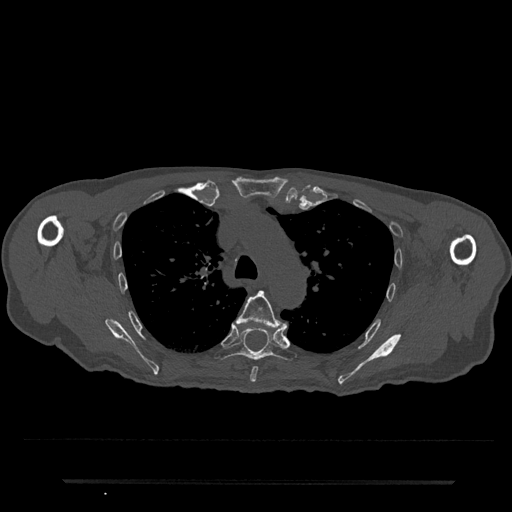
CT including the spine, one axial slice. Reconstruction kernel Br40s/3. Bone window (W 1800 / L 400 HU). 0.5 mm slice thickness. 512 × 512 image matrix. Male patient, age 74 years. From the clinical record (not read from this slice): primary cancer: prostate.
Outlined on this slice (semi-automatic segmentation, software-assisted and operator-edited):
- T5 vertebra: bounding box (x1, y1, x2, y2) in pixels: (236, 290, 288, 382)
- T6 vertebra: (215, 328, 297, 362)